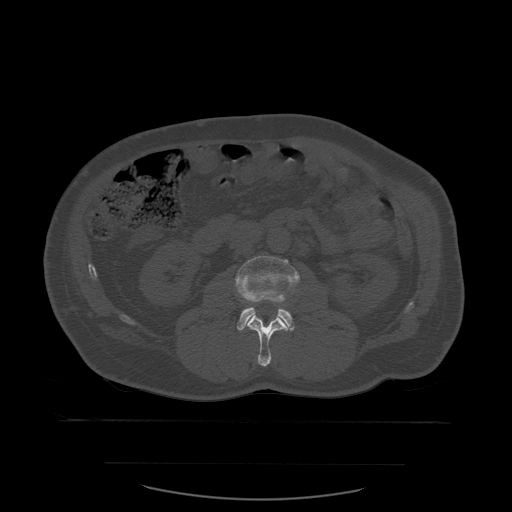
CT including the spine, one axial slice. Position 205 of 590 along the scan axis. Bone window (W 1800 / L 400 HU). 1.25 mm slice thickness. 512 × 512 image matrix, field of view 479 × 479 mm. Patient age 71 years. From the clinical record (not read from this slice): primary cancer: lung.
Structures marked on this image (semi-automatic segmentation, software-assisted and operator-edited):
- L2 vertebra: bounding box (x1, y1, x2, y2) in pixels: (246, 314, 291, 367)
- L3 vertebra: (235, 256, 300, 331)